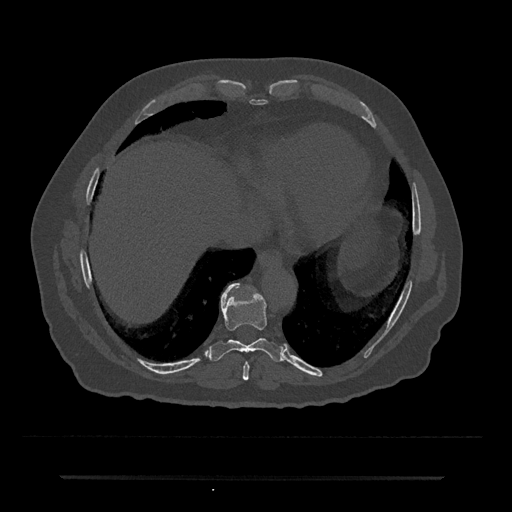
CT including the spine, one axial slice. Slice 280 of 797 in the series (ordered by position). Reconstruction kernel Br40s/3. 120 kVp. Bone window (W 1800 / L 400 HU). 0.5 mm slice thickness. 512 × 512 image matrix, field of view 437 × 437 mm. Male patient, age 69 years. From the clinical record (not read from this slice): primary cancer: prostate.
Outlined on this slice (semi-automatic segmentation, software-assisted and operator-edited):
- T8 vertebra: bounding box <242,362,249,380> (left, top, right, bottom; pixels)
- T9 vertebra: <210,283,284,362>